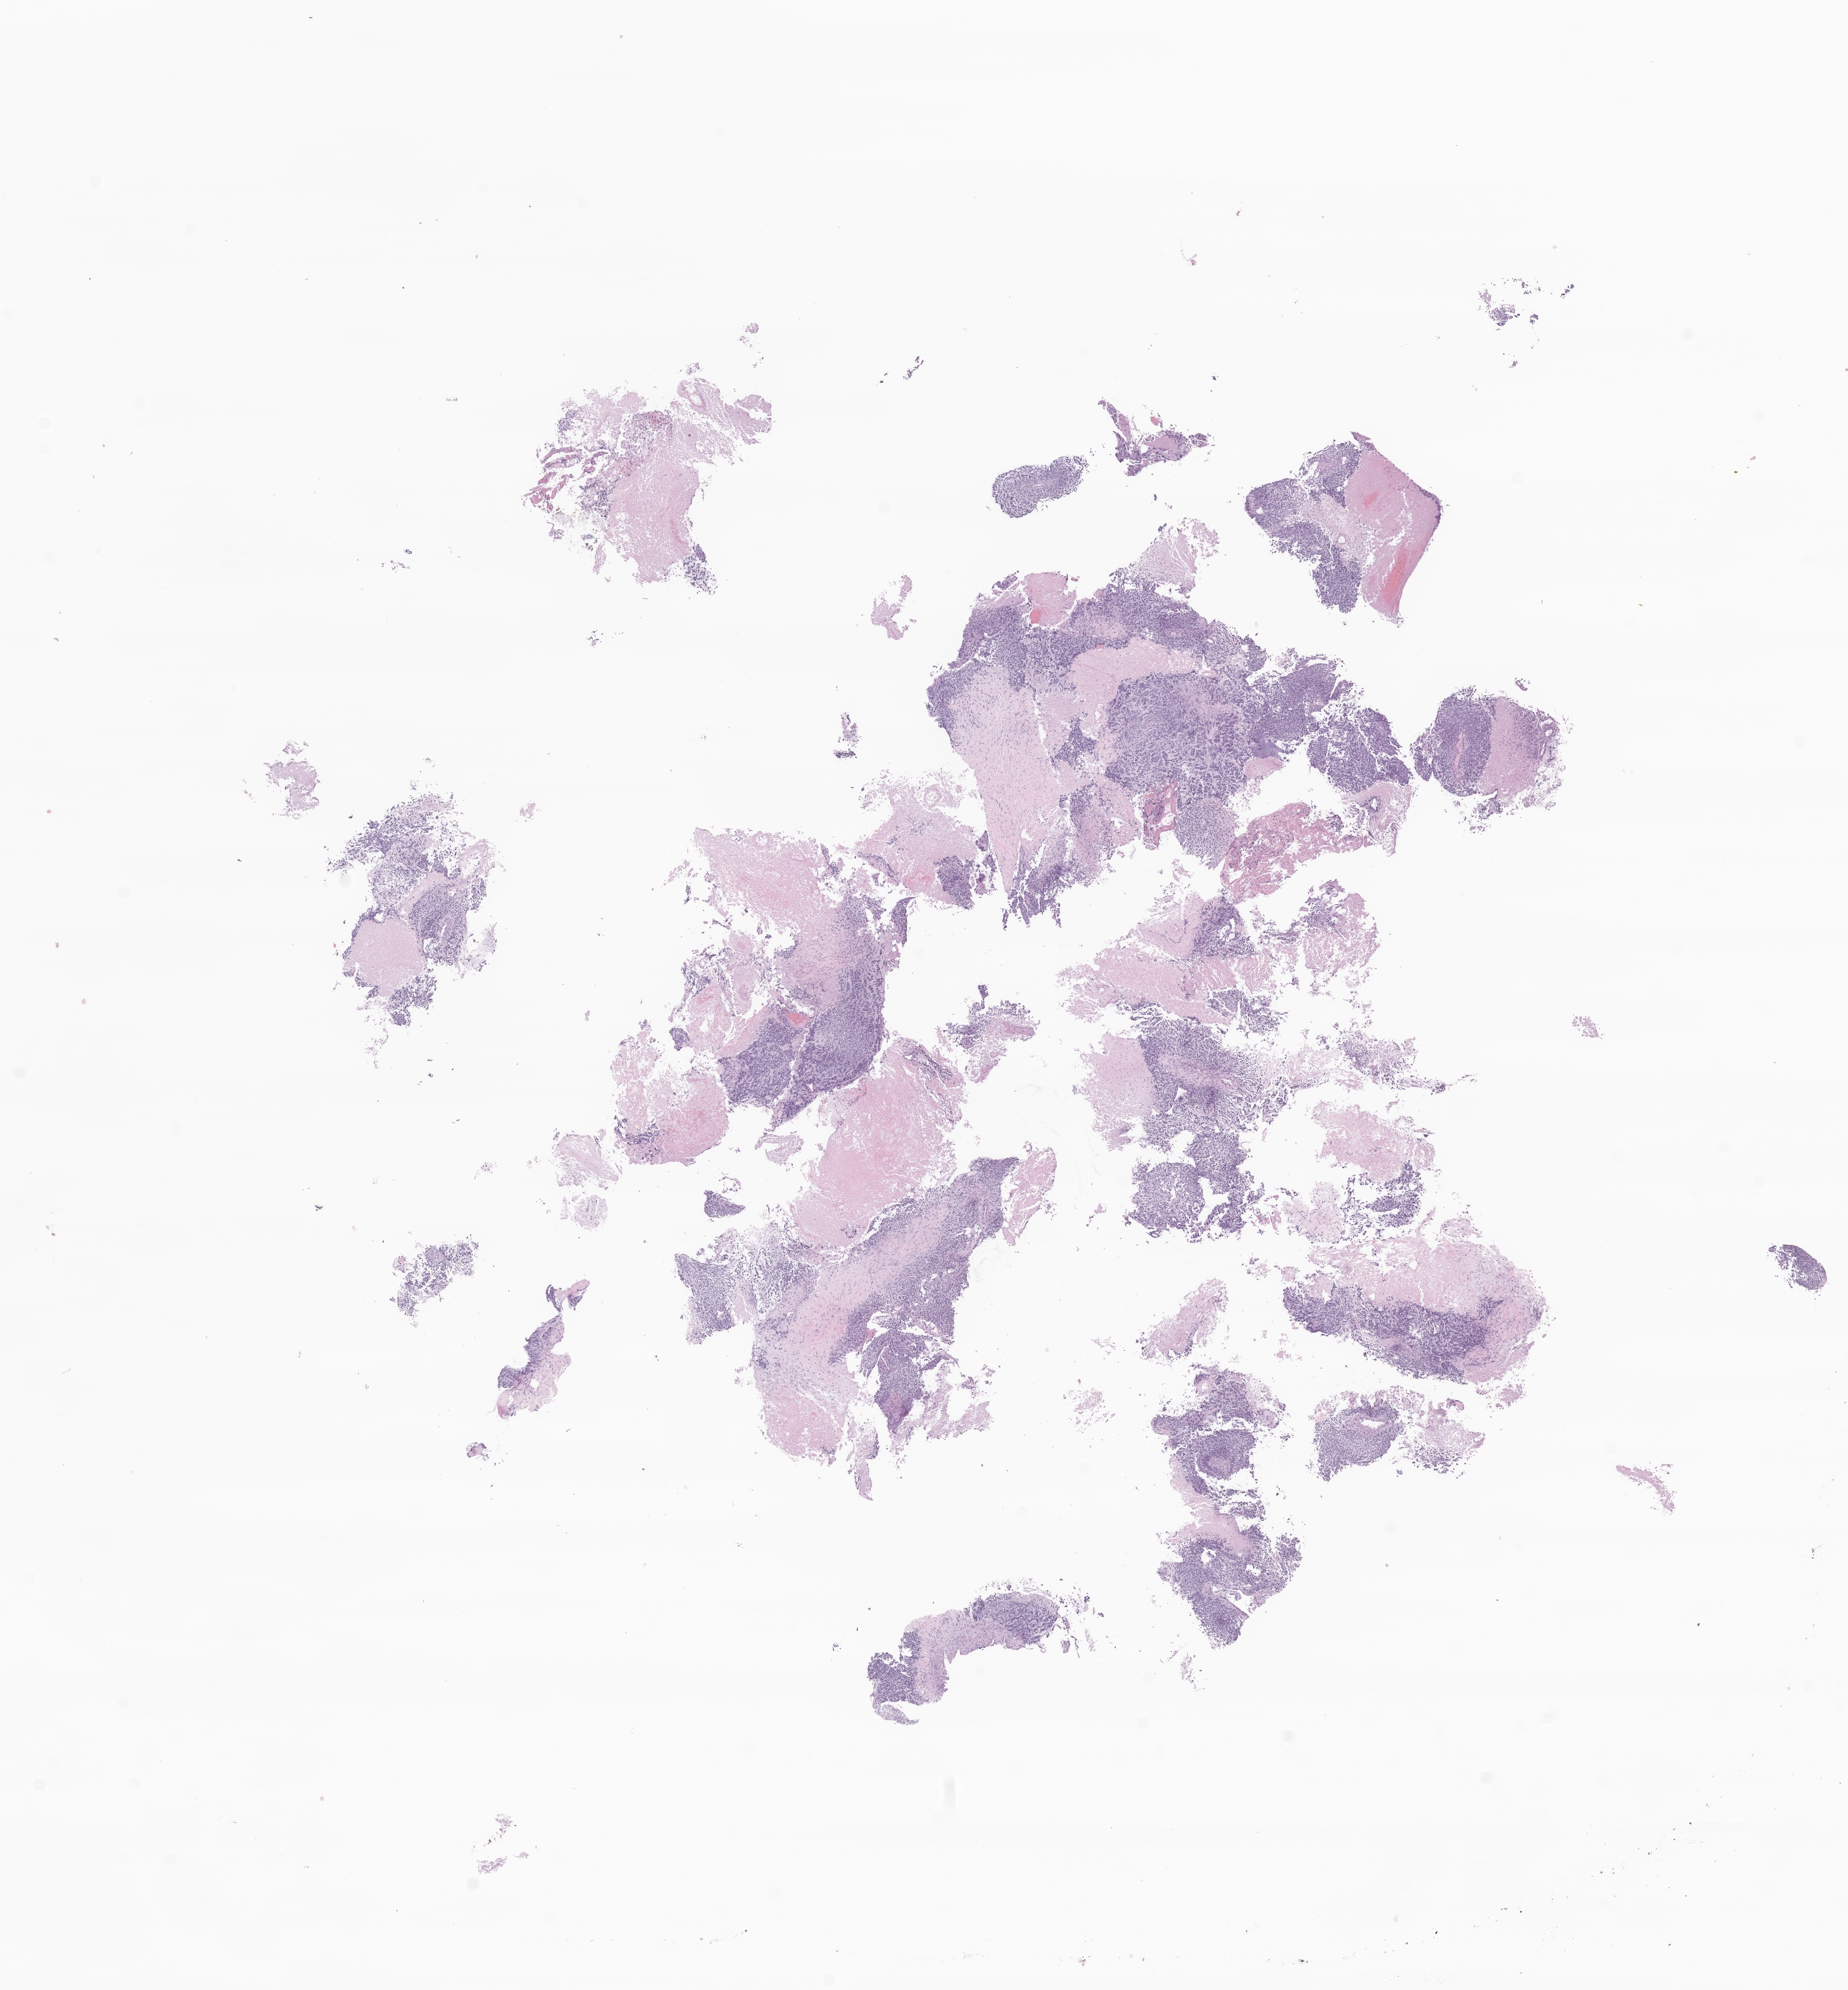
Hematoxylin and eosin (H&E) whole-slide image of tumor tissue from the soft tissue of pelvis — a low-resolution overview of the entire scanned area, about 13.2 x 14.2 mm; formalin-fixed, paraffin-embedded (FFPE) tissue. Patient male; age 112 months (9 years 4 months).
Diagnosis: Malignant peripheral nerve sheath tumor, NOS.